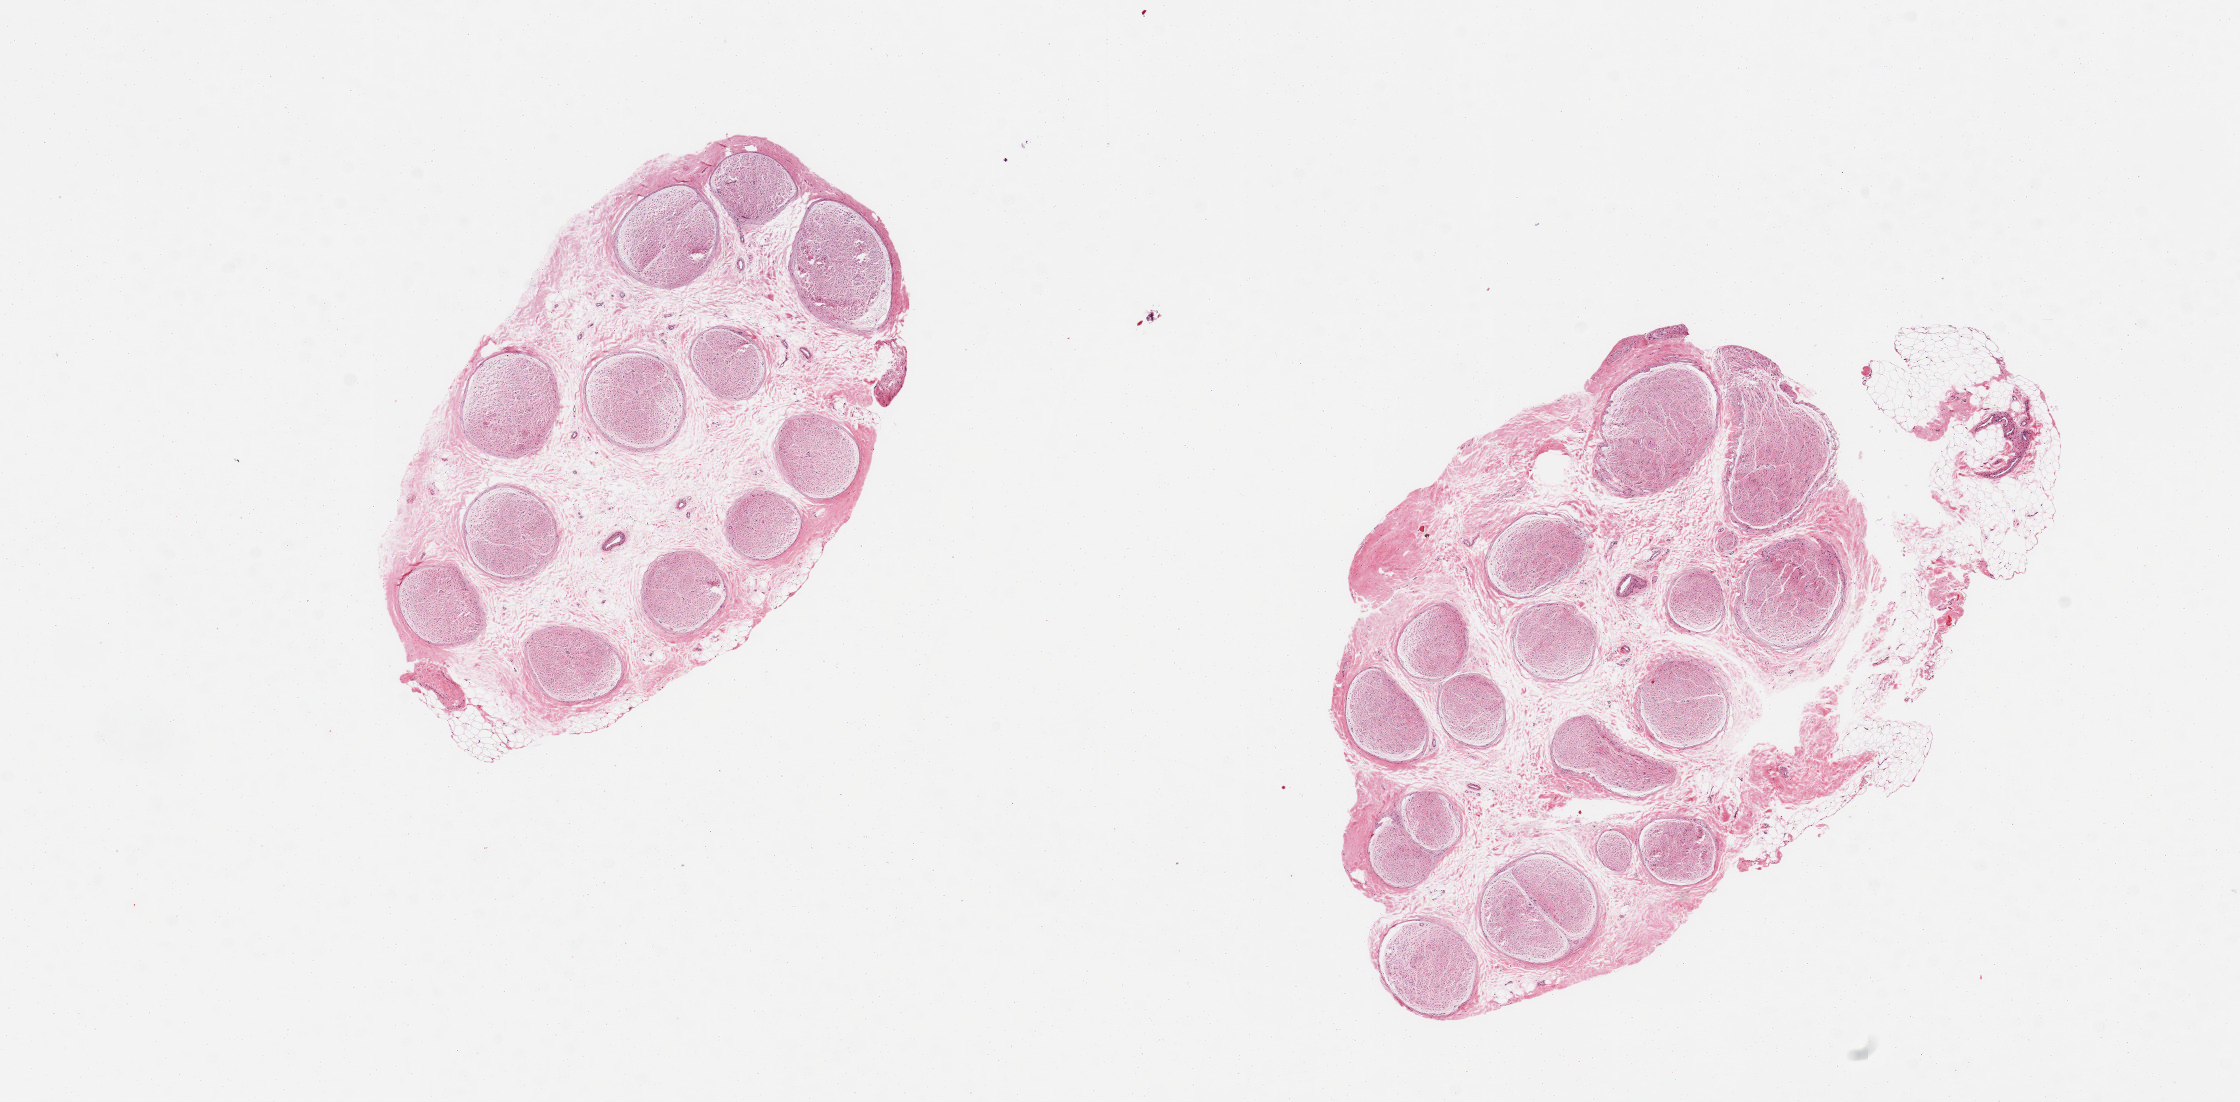
Whole-slide image, haematoxylin and eosin stain, whole scanned area (about 17.7 x 8.7 mm, from a 20x scan) shown as a low-resolution overview; PAXgene-fixed, paraffin-embedded tissue; sampled site (target tissue): tibial nerve; tissue donor sample. Donor: male.
Review note (as recorded): 2 pieces, minimal adherent fat.